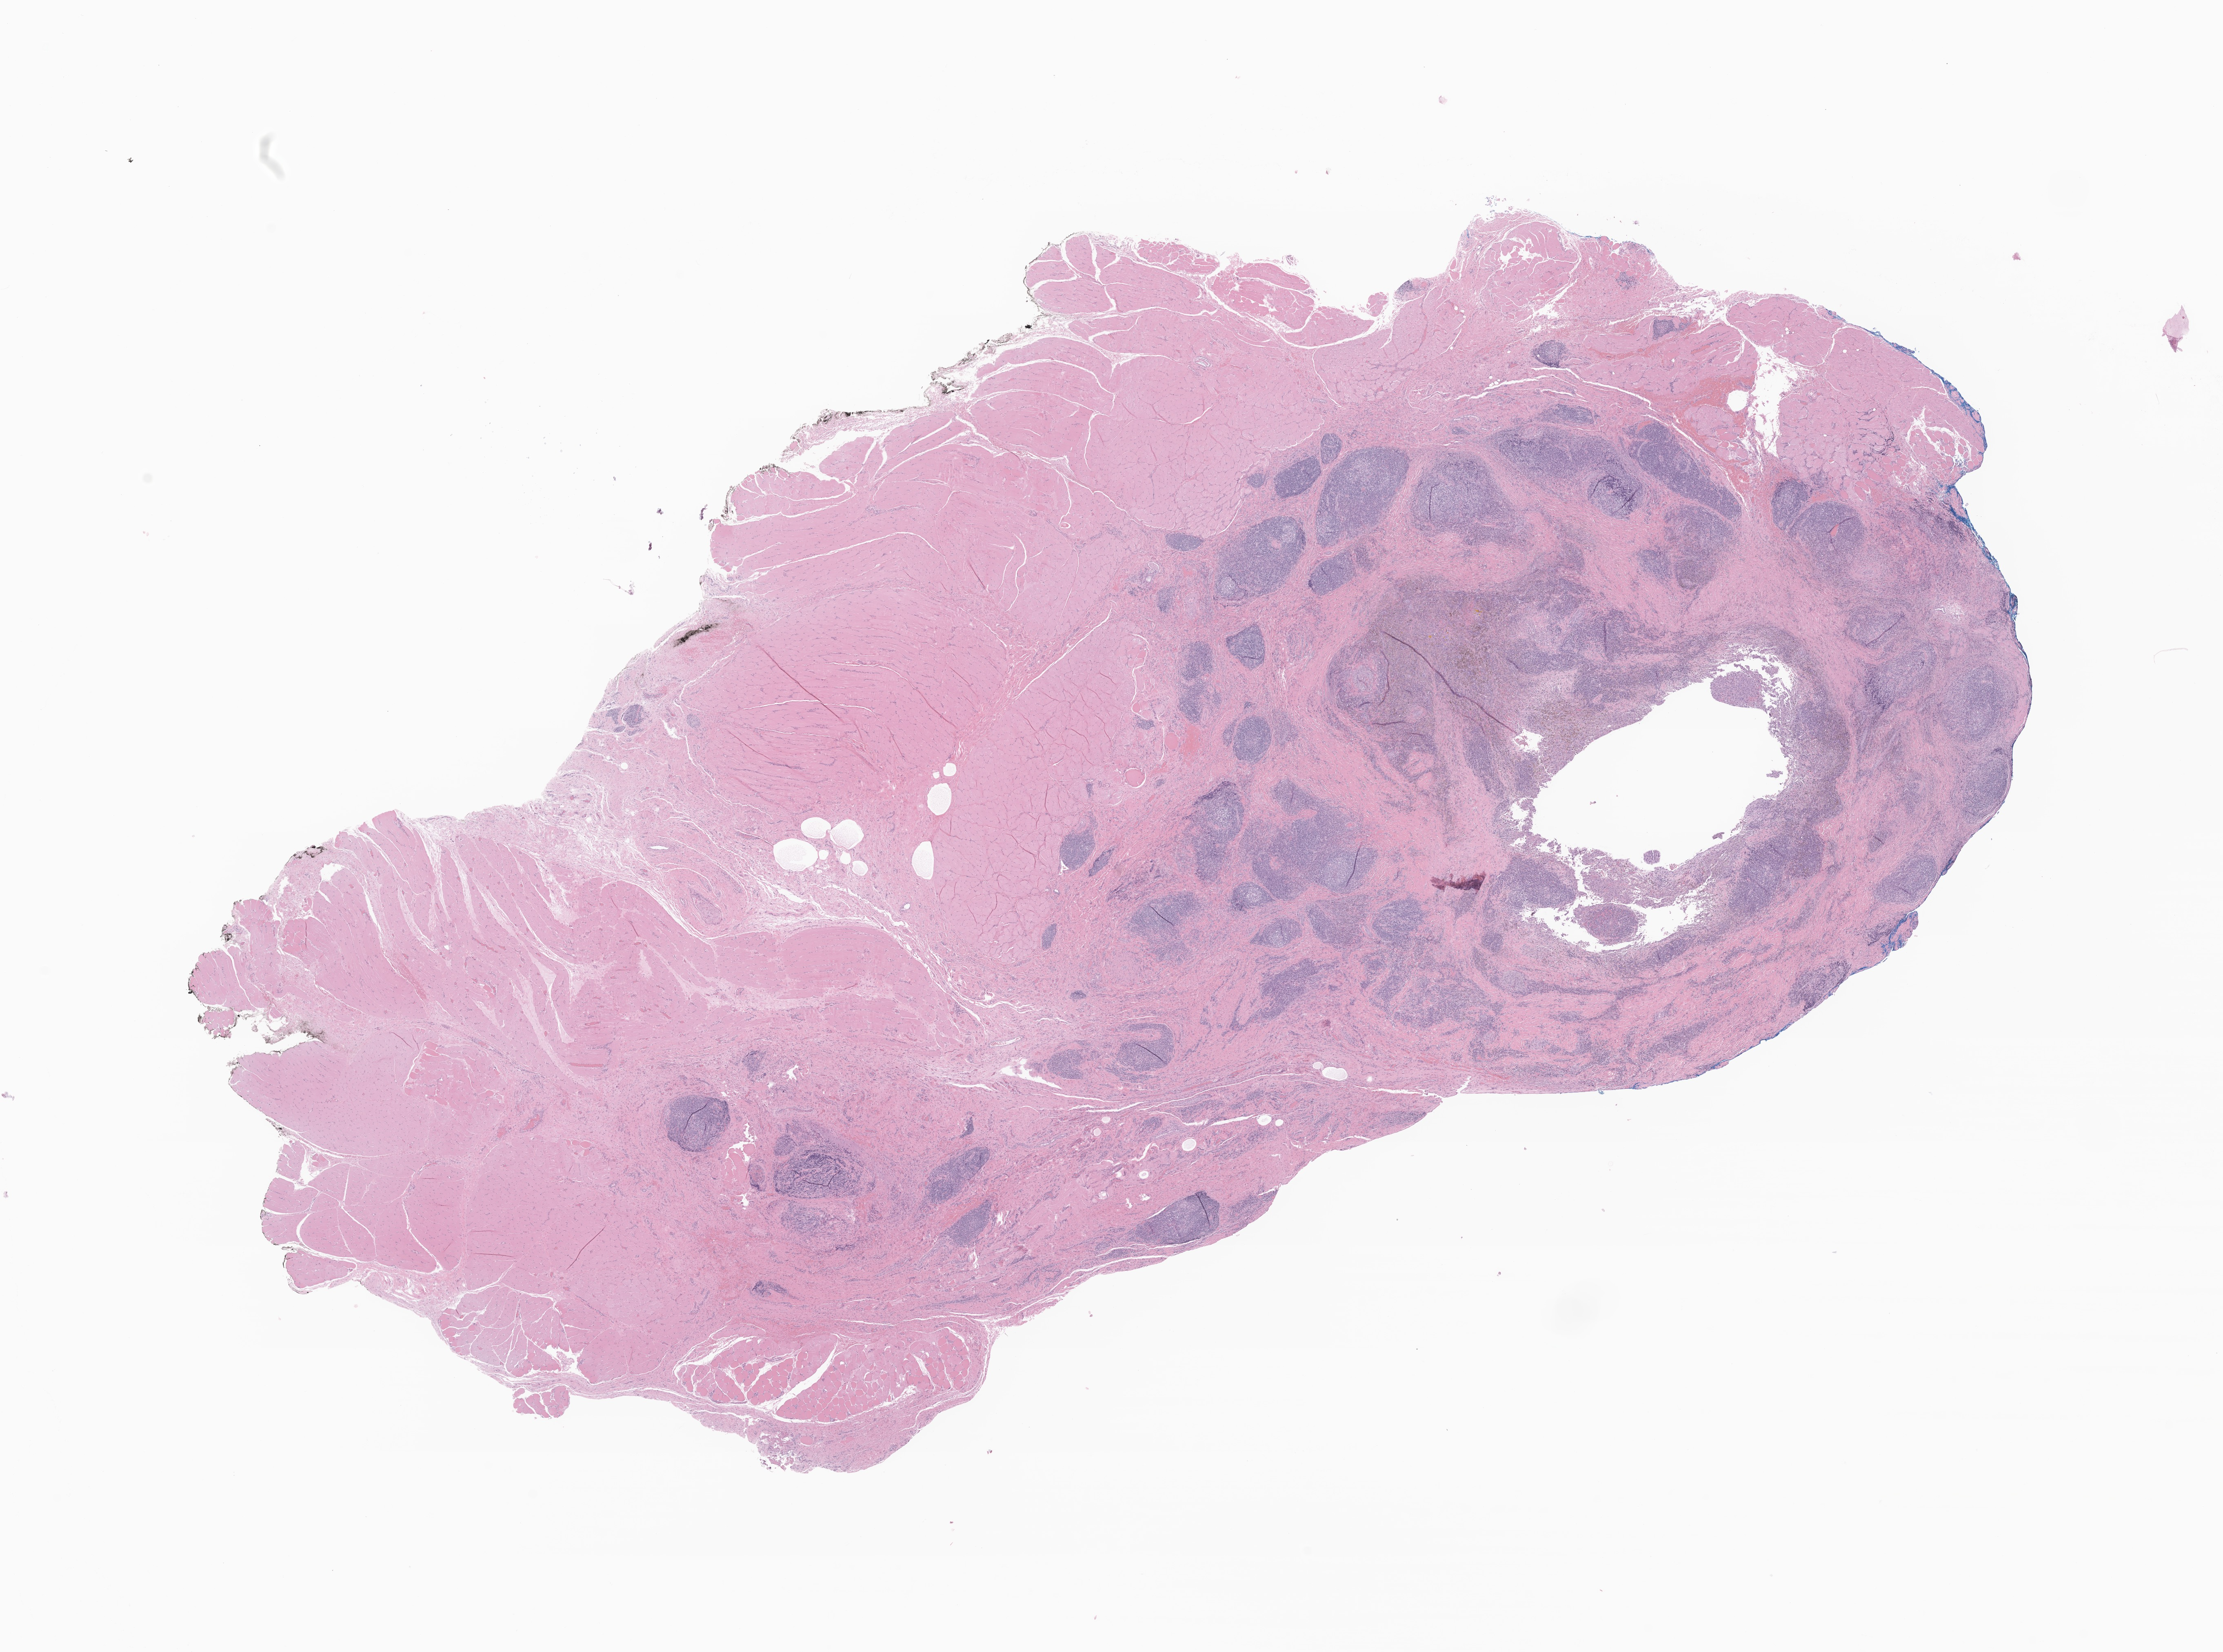
Digitized haematoxylin and eosin-stained section of tumor tissue from the soft tissue of thorax — low-resolution overview of the scanned area, about 23.0 x 17.1 mm; FFPE section. Male patient, age 117 months (9 years 9 months).
Diagnosis (ICD-O-3 morphology term): Angiomatoid fibrous histiocytoma.